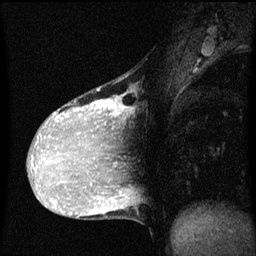
Breast MRI (dynamic contrast-enhanced), one sagittal slice; position 28 of 60 along the scan axis; dynamic contrast-enhanced series, image 2 of 3 at this slice position (ordered by acquisition); 1.5 T; TE 4.2 ms, TR 8 ms; 256 × 256 image matrix. Patient: female, 36 years.
Annotated regions visible in this slice (semi-automatically segmented with operator editing):
- analysis volume of interest (the breast-tissue region the enhancement analysis was run in; not a lesion): box from (x=33, y=76) to (x=131, y=169) px
- tumour enhancement mask (voxels above the 70 % enhancement threshold inside the analysis volume of interest): (x=33, y=98)–(x=131, y=169)